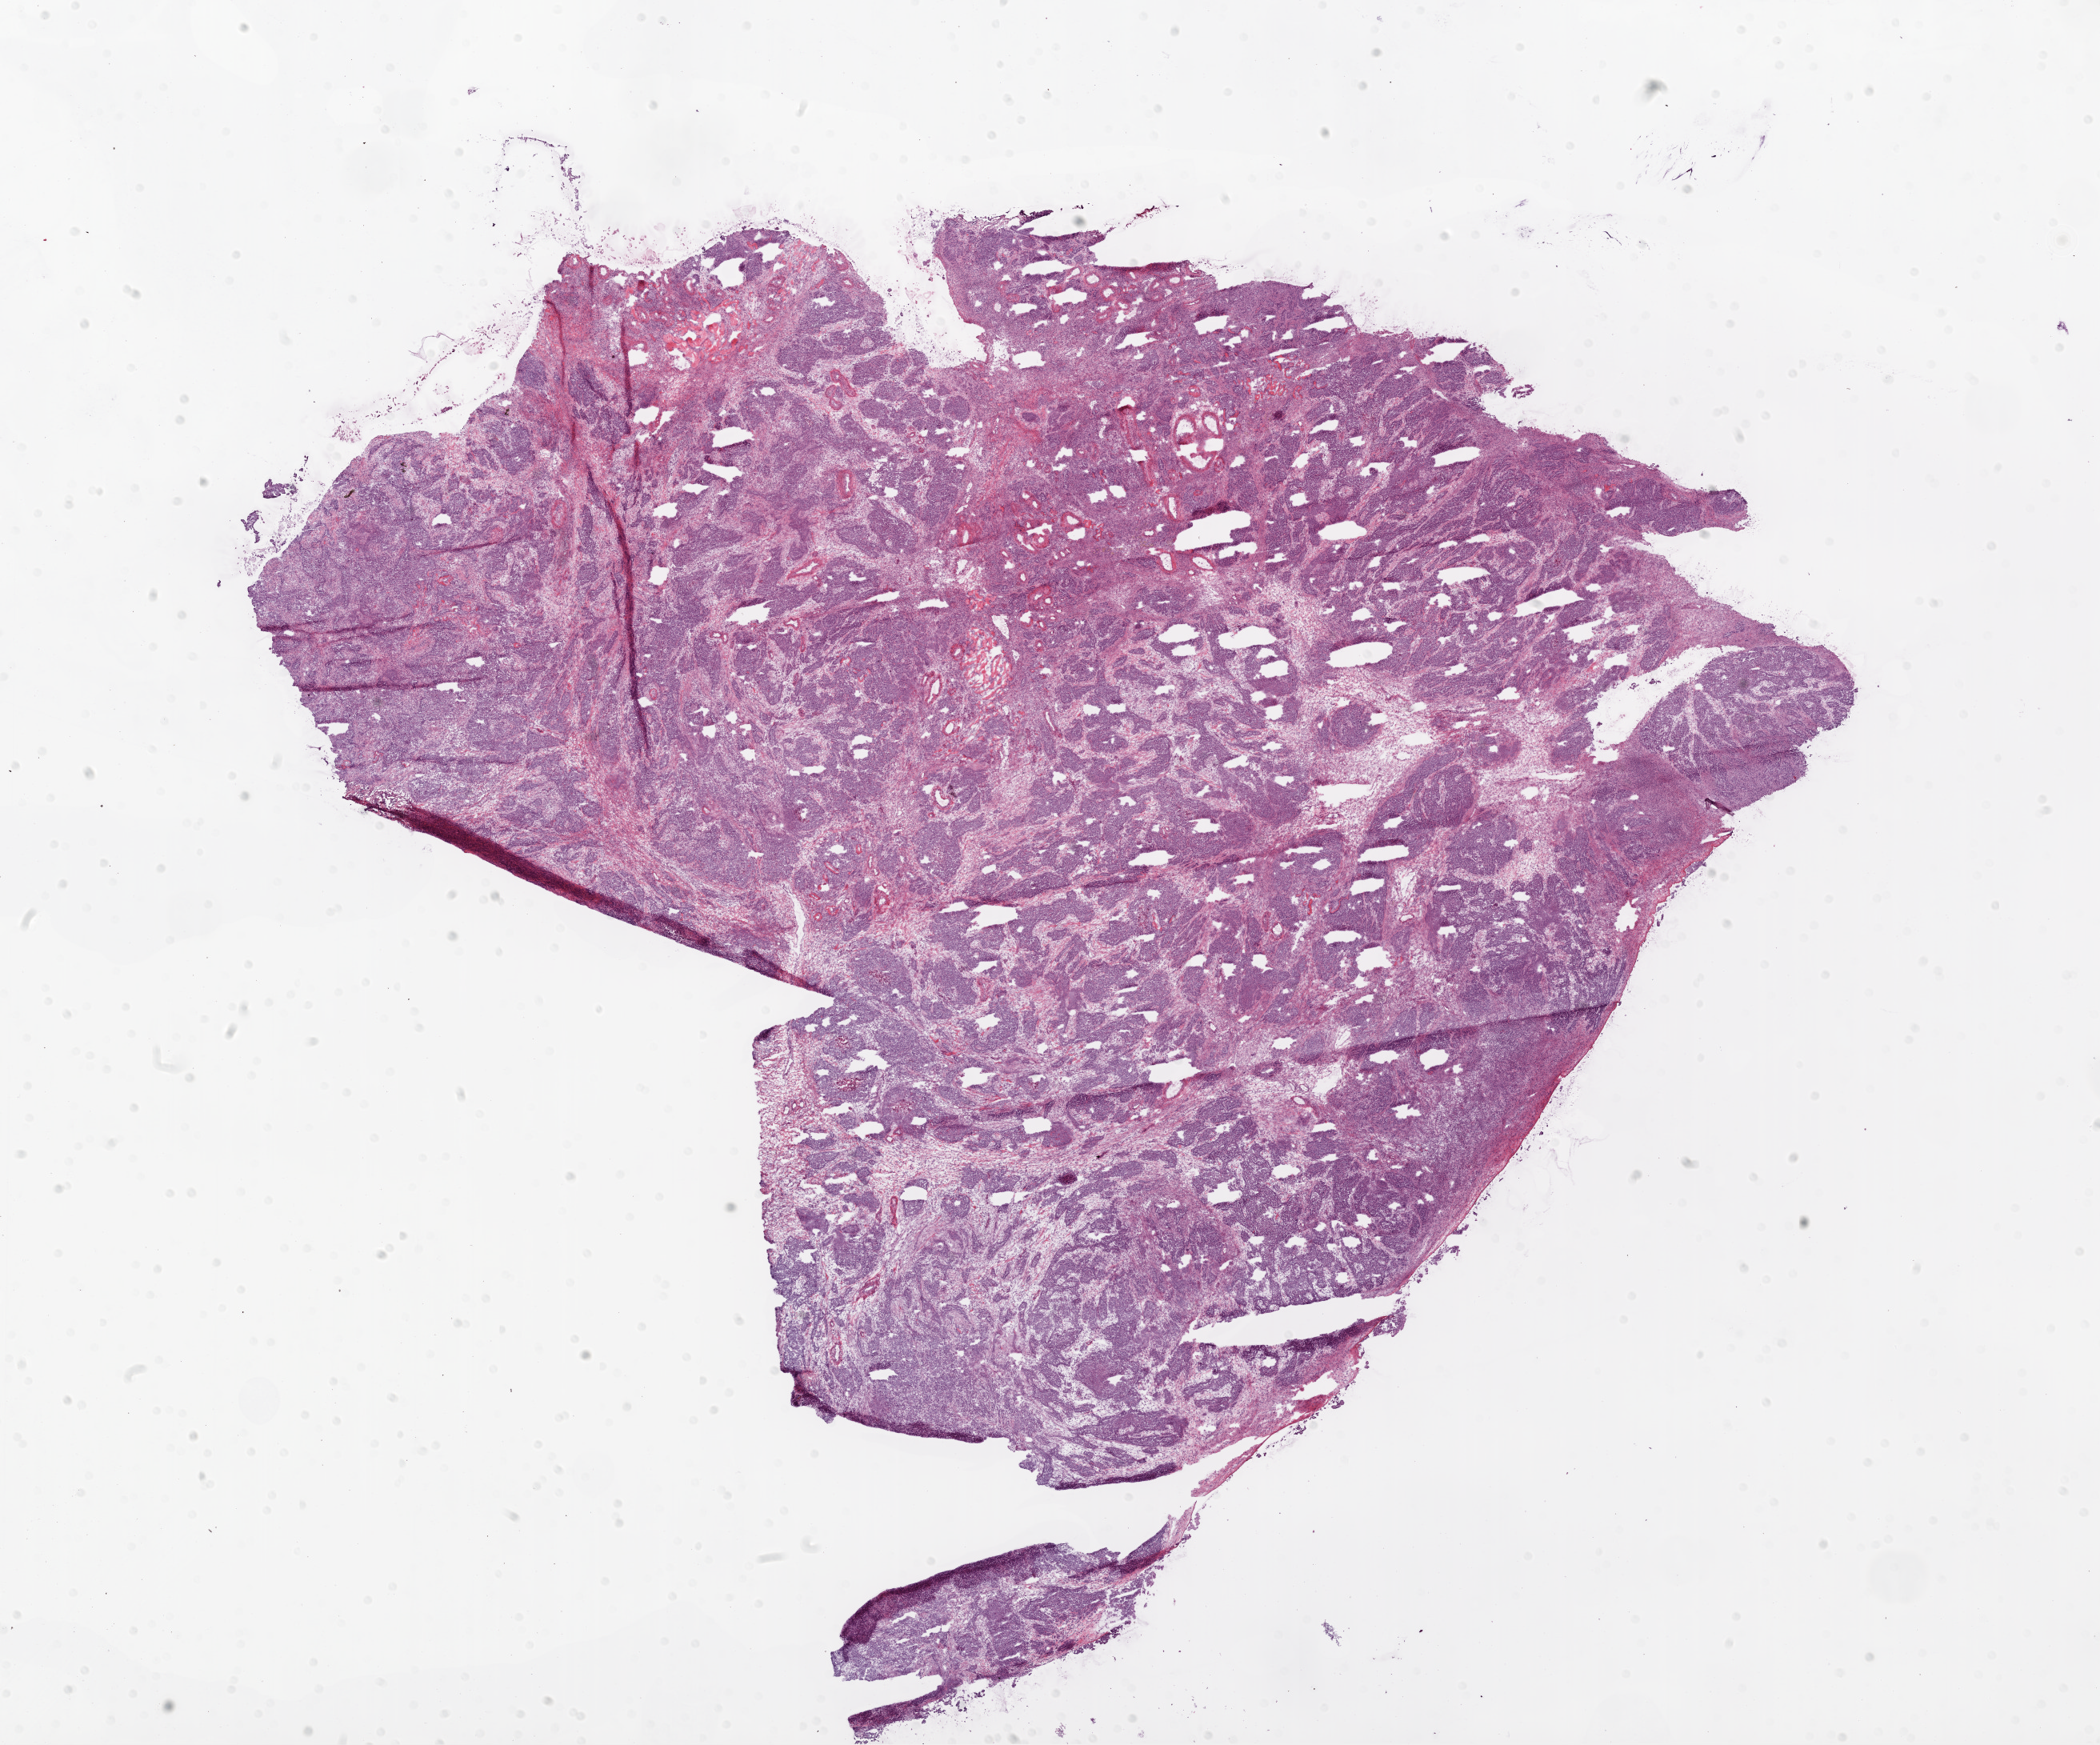
H&E-stained whole-slide image — low-resolution overview of the scanned area, about 21.1 x 17.5 mm. Frozen section. Ovary, primary tumour sample. Female, age 53 years at initial diagnosis. Histologic grade: G2 (moderately differentiated). Pathologist review of this section (percent, as recorded): tumour cells 85%, tumour nuclei 95%, normal cells 7%, stromal cells 5%, necrosis 3%.
Laterality: bilateral. FIGO stage: IIIC. Diagnosis: Serous cystadenocarcinoma, NOS.